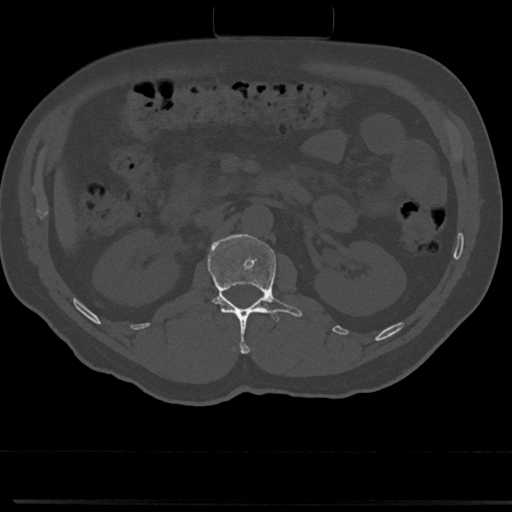
CT including the spine, one axial slice. Slice 74 of 817 in the series (ordered by position). 120 kVp. Bone window (W 1800 / L 400 HU). 512 × 512 image matrix. Male patient, age 61 years. Case-level facts recorded for this patient, not image findings: primary cancer: prostate.
Outlined on this slice (semi-automatically segmented with operator editing):
- L1 vertebra: bounding box (x1, y1, x2, y2) in pixels: (191, 235, 301, 352)